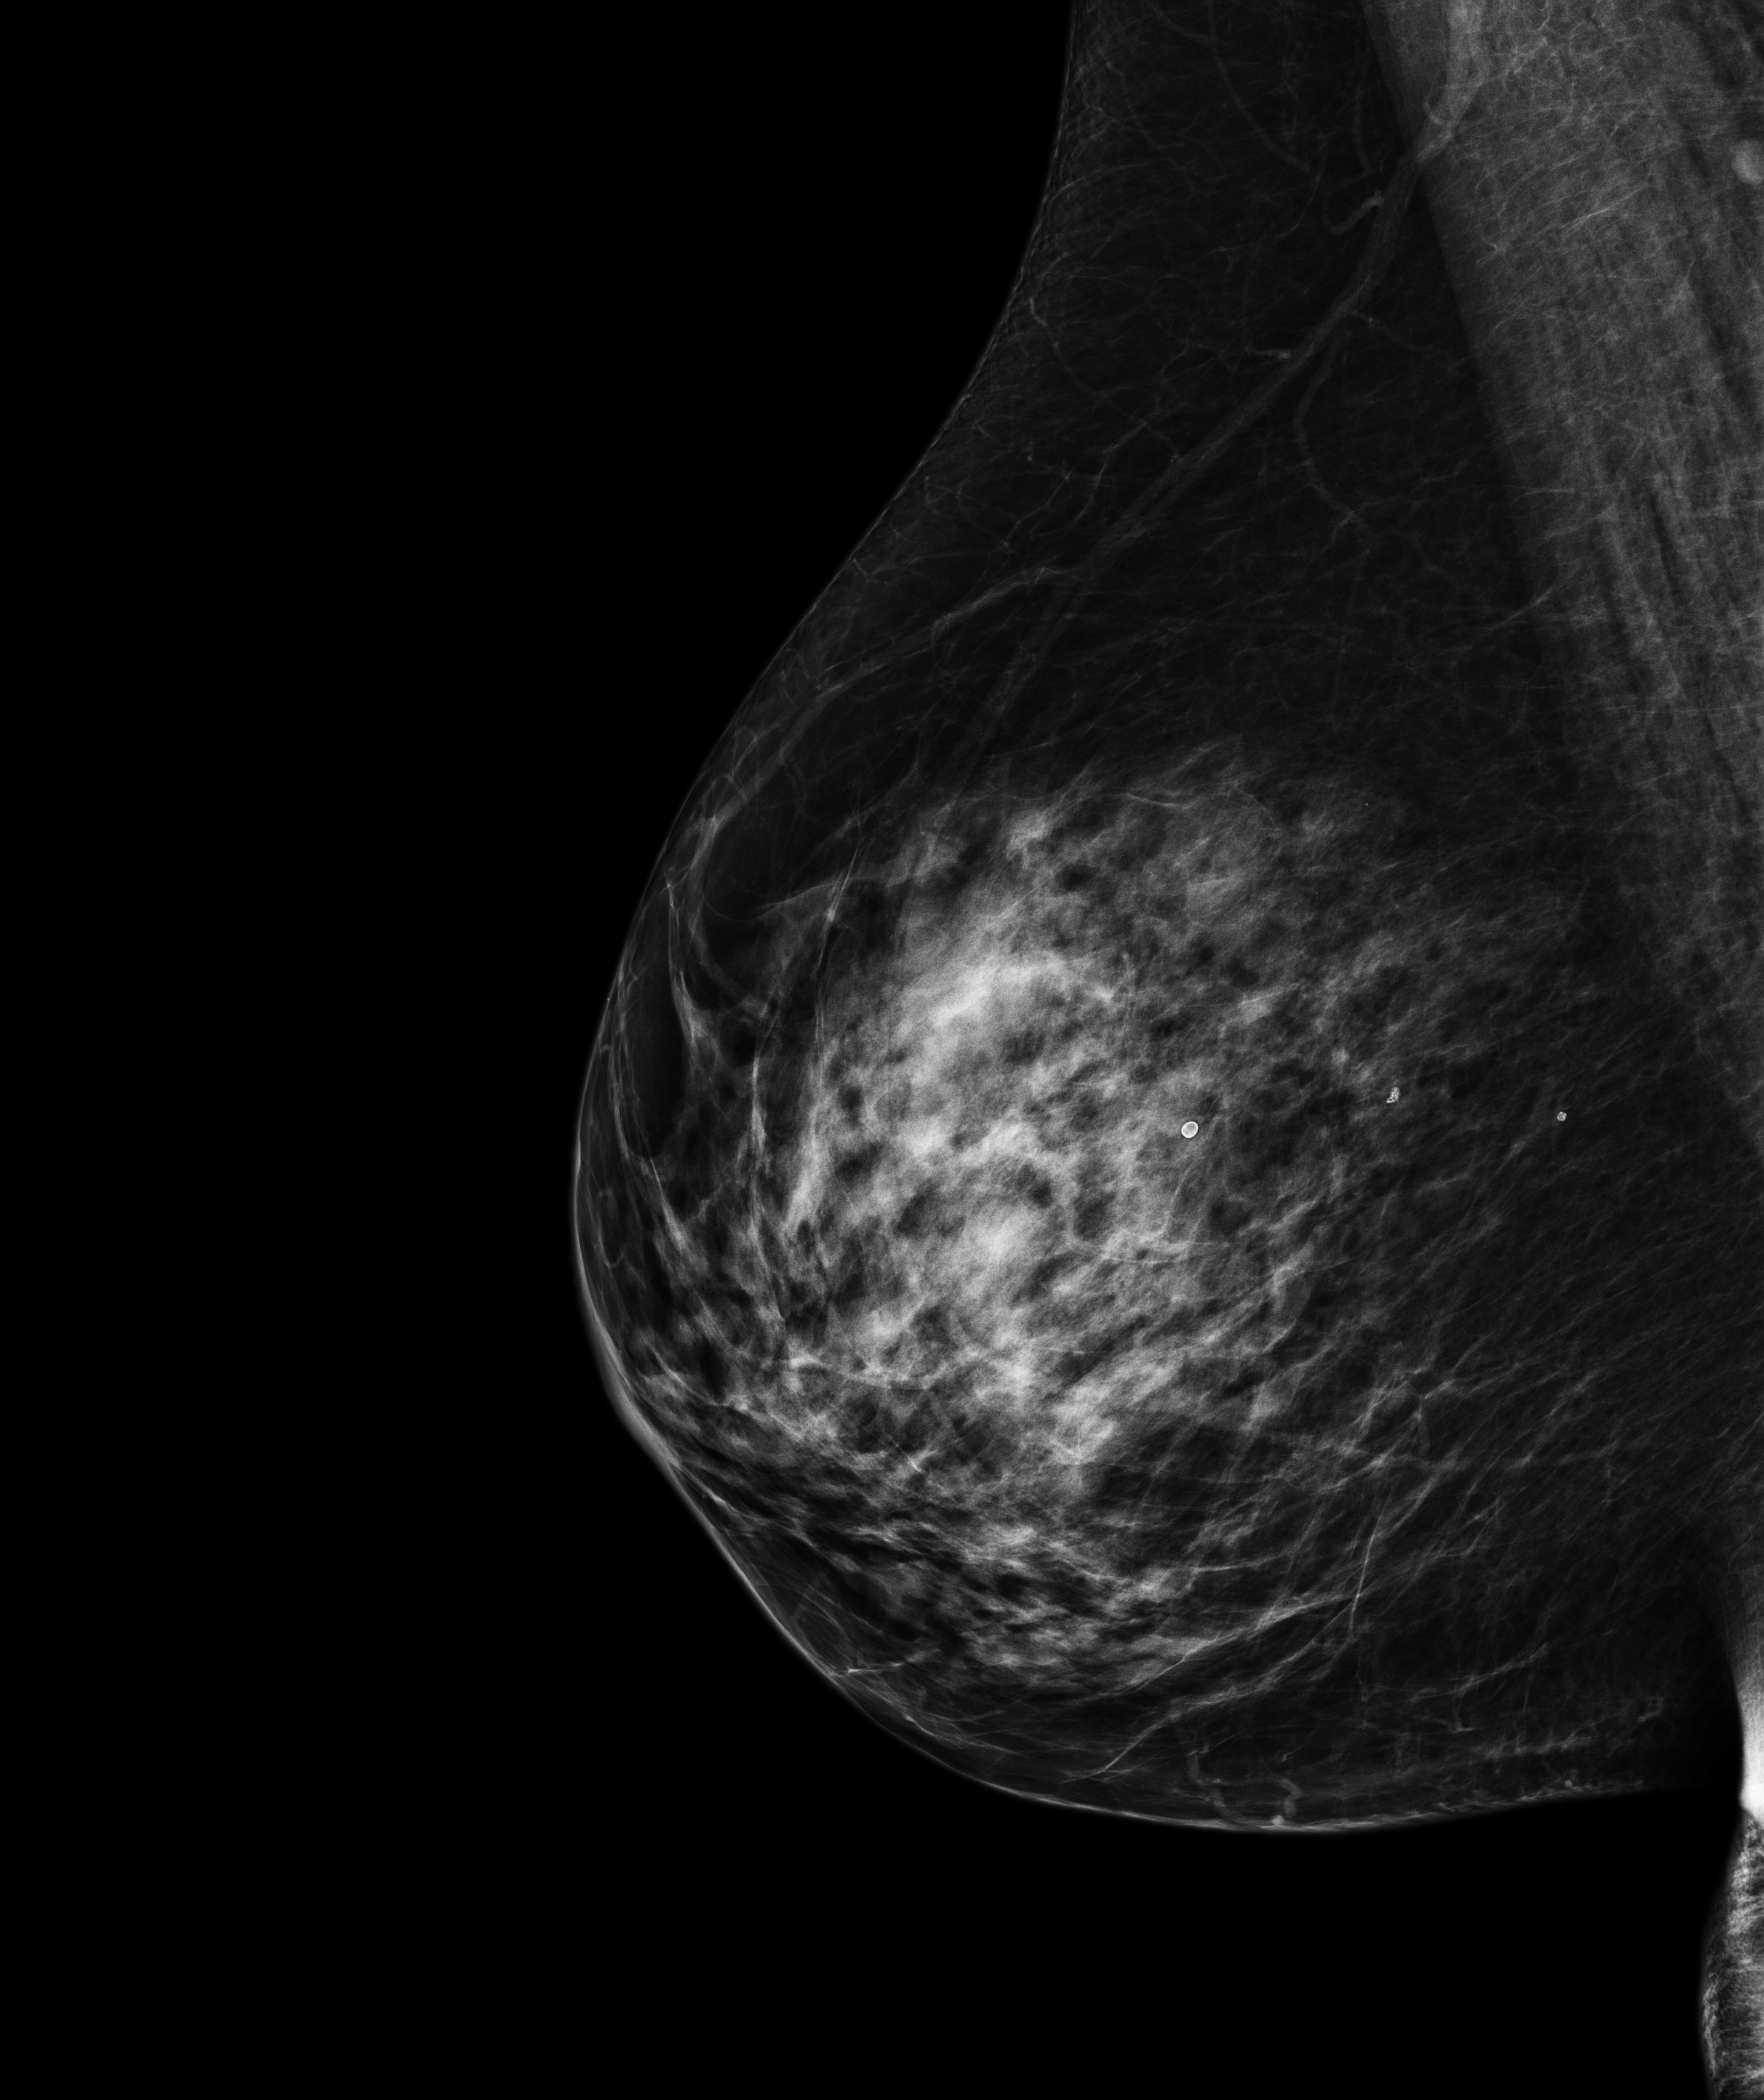
Annual screening mammography examination; compressed breast thickness 60.8 mm; system: Senographe Pristina. Patient aged 66 years (female).
Image type: full-field digital mammogram. Breast: right. Projection: mediolateral oblique (MLO) view.